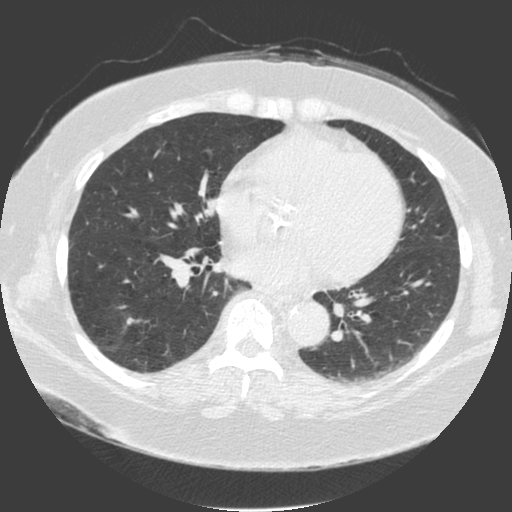
Low-dose screening chest CT, one axial slice. Position 81 of 175 along the scan axis. 120 kVp. Lung window (W 1500 / L -600 HU). 512 × 512 image matrix, field of view 370 × 370 mm.
Annotated regions visible in this slice (outlined manually by an expert reader):
- lesion 1 (tumor, lower lobe of right lung): bounding box (x1, y1, x2, y2) in pixels: (127, 318, 134, 324)